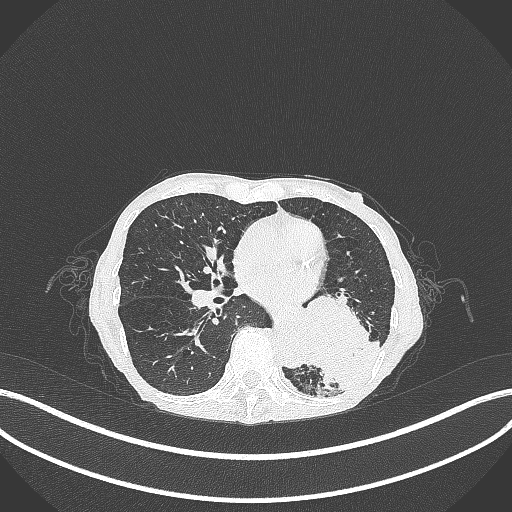
Chest CT, one axial slice. Reconstruction kernel B70f. 120 kVp. Lung window (W 1500 / L -600 HU). 1 mm slice thickness. 512 × 512 image matrix, field of view 400 × 400 mm. Patient: female, 70 years. Case-level facts recorded for this patient, not image findings: clinical TNM (as recorded): T3 N0 M0.
Outlined on this slice (rectangle marked by the reading radiologist):
- lung tumour (recorded histology: small cell carcinoma): box from (x=298, y=286) to (x=385, y=394) px